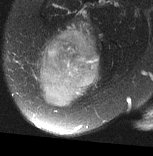
MRI of an extremity soft-tissue mass, one axial slice; position 25 of 77 along the scan axis; T2-weighted fat-saturated; MR volume resampled by the dataset authors to the PET/CT grid (not the native acquisition matrix); 3.27 mm slice thickness; 153 × 156 image matrix. Female patient. Case-level facts recorded for this patient, not image findings: histological type: synovial sarcoma; grade: intermediate; site of the primary tumour: right buttock.
Annotated regions visible in this slice (expert contour drawn on MRI and transferred to this co-registered scan by the dataset authors):
- gross tumour volume including surrounding oedema: bounding box [x1, y1, x2, y2] px = [33, 22, 100, 107]
- gross tumour volume (mass): [37, 27, 100, 107]